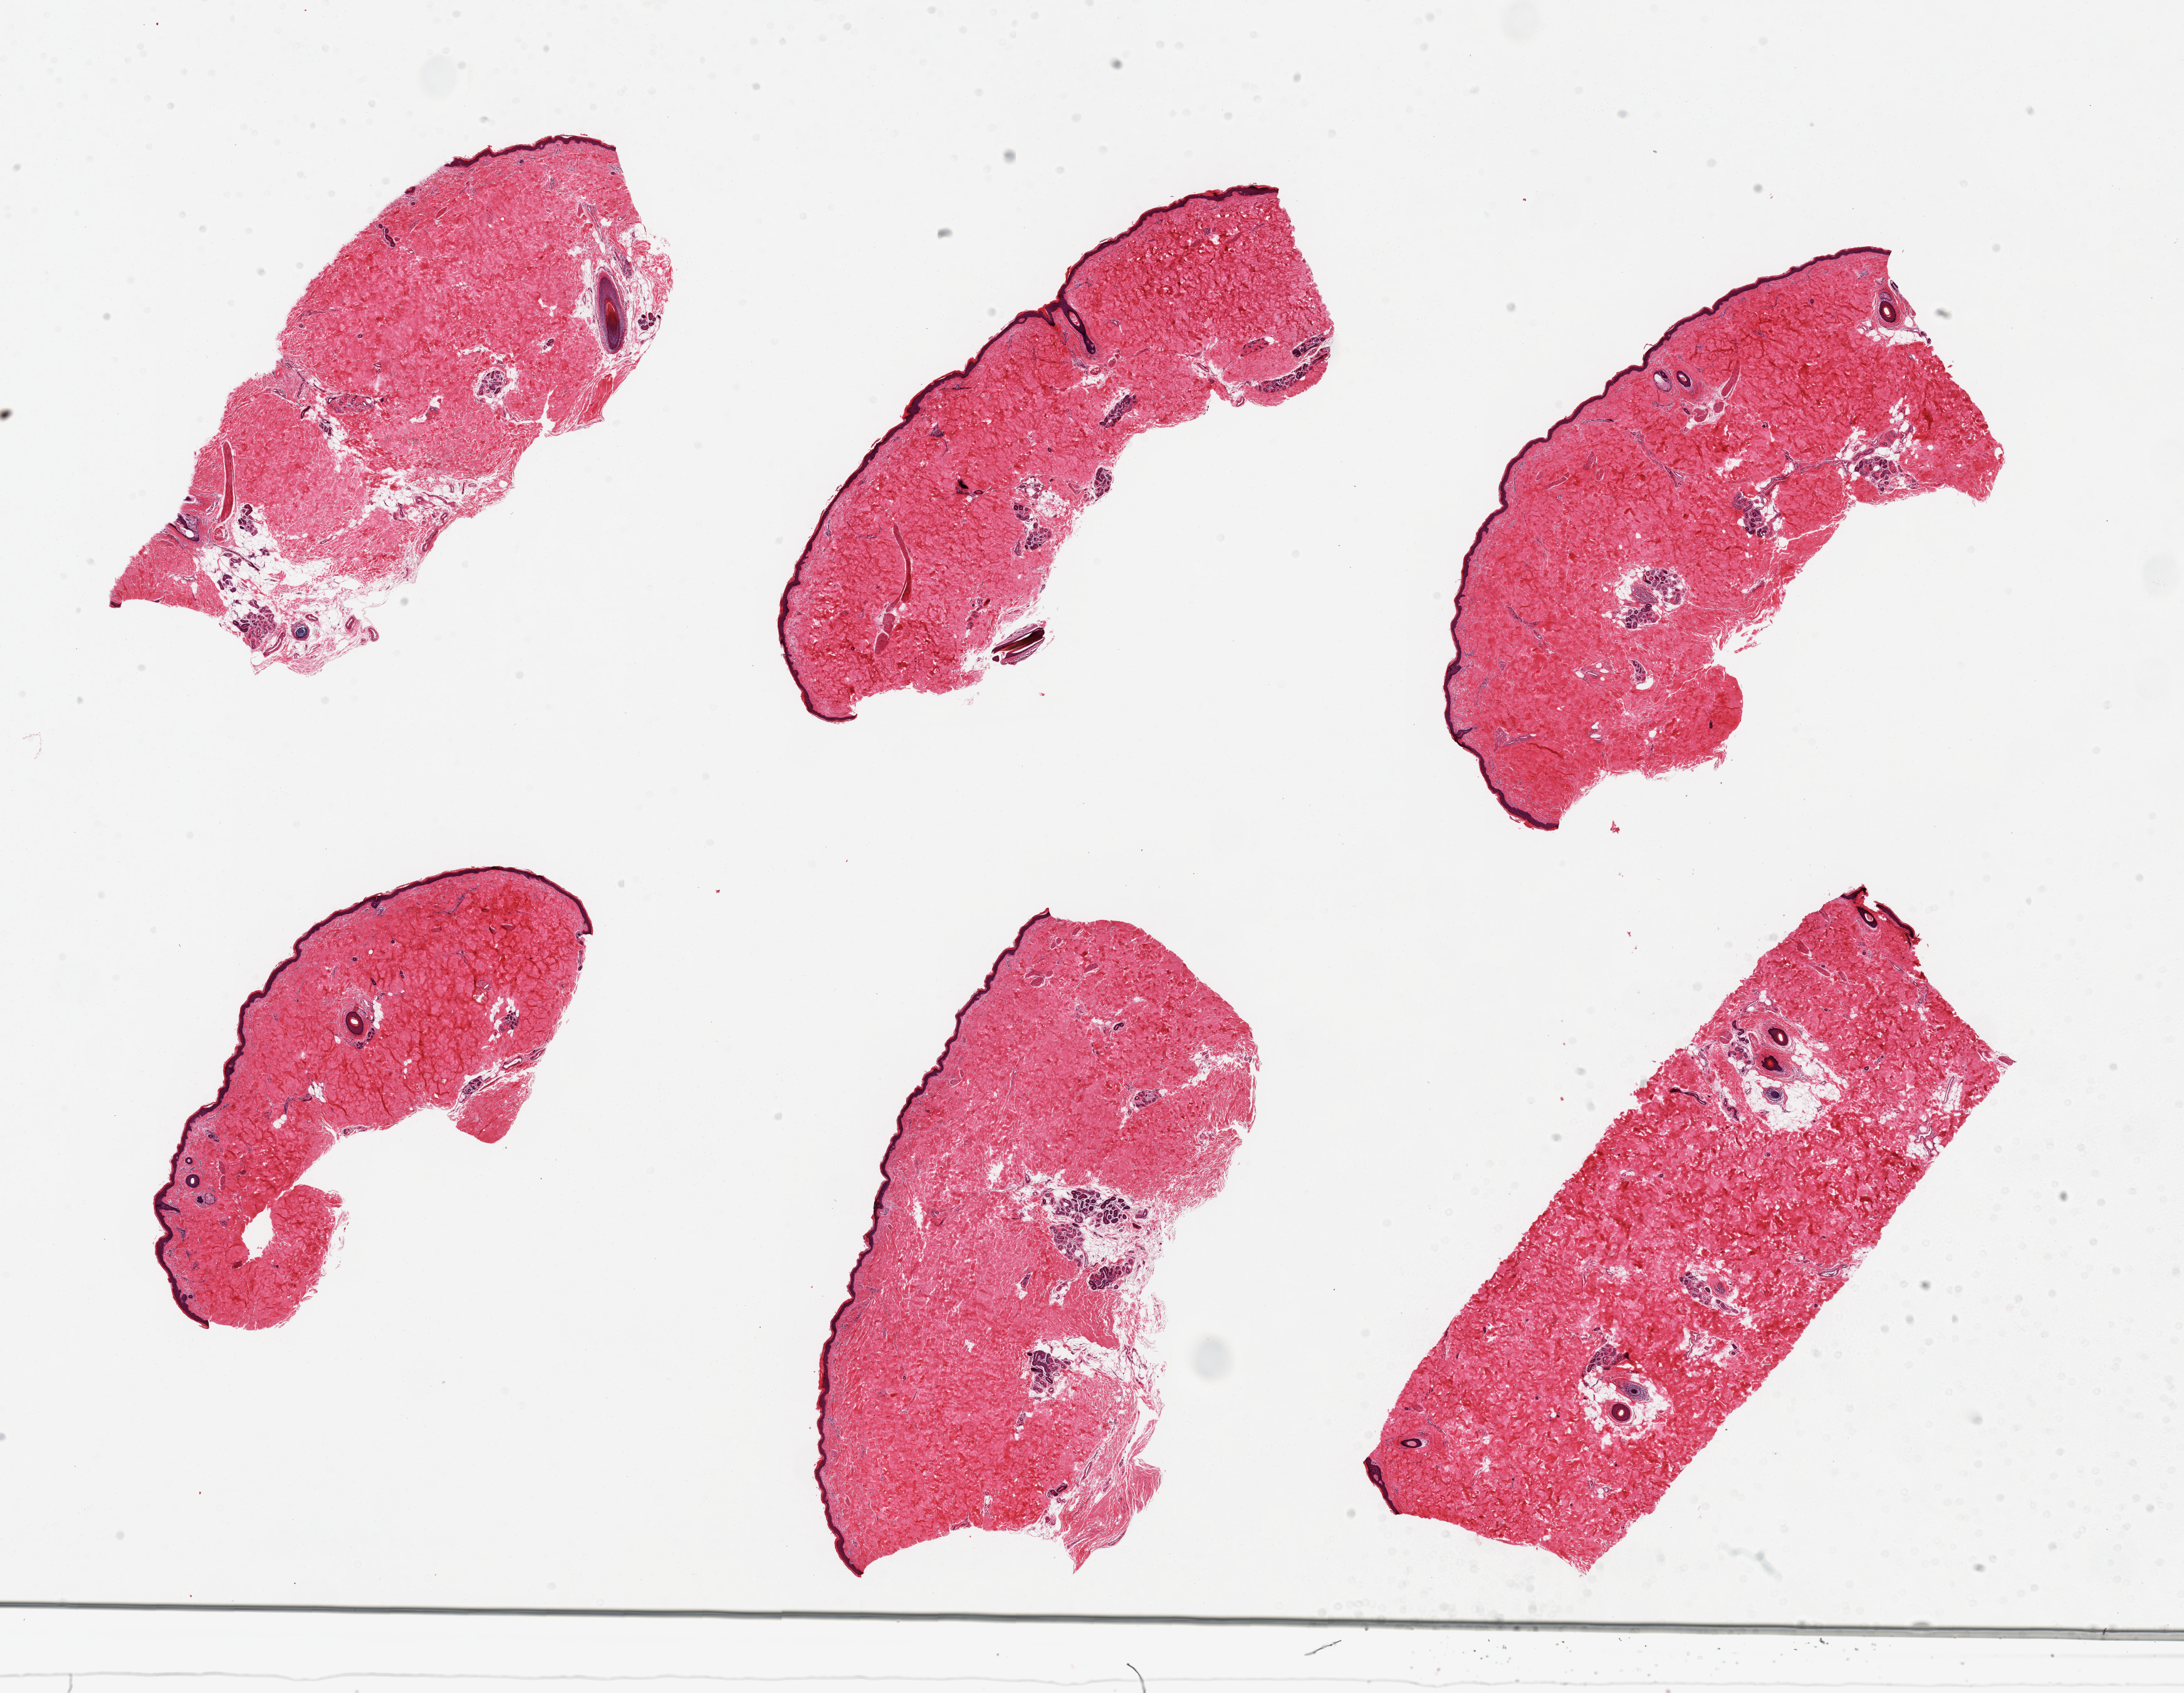
H&E whole-slide image — low-resolution overview of the scanned area, about 27.6 x 21.4 mm. PAXgene-fixed, paraffin-embedded tissue. Sampled site (target tissue): skin of lower leg. Donor tissue sample.
• reviewer comment on this tissue sample: 6 pieces;well trimmed; 10% intradermal fat